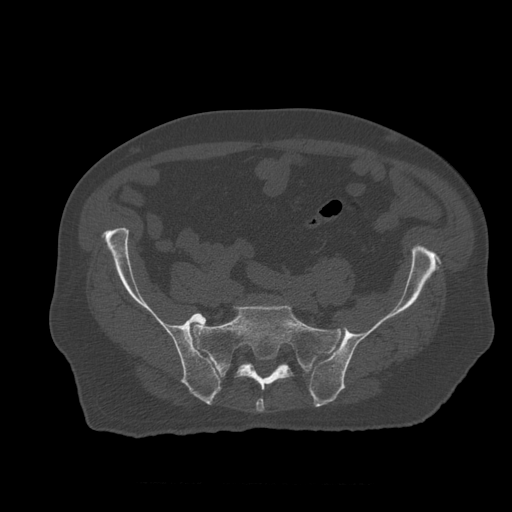
CT including the spine, one axial slice; reconstruction kernel STANDARD; bone window (W 1800 / L 400 HU); 1.25 mm slice thickness; 512 × 512 image matrix. Patient age 73 years. From the clinical record (not read from this slice): primary cancer: prostate.
Outlined on this slice (semi-automatically segmented with operator editing):
- L5 vertebra: bounding box <213,368,218,375> (left, top, right, bottom; pixels)